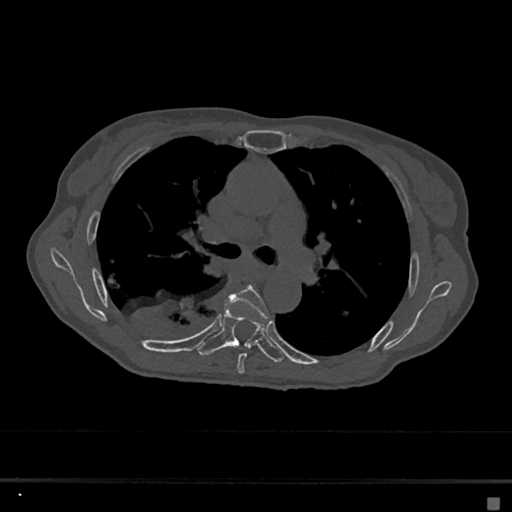
CT including the spine, one axial slice; slice 437 of 797 in the series (ordered by position); reconstruction kernel Br40s/3; 120 kVp; bone window (W 1800 / L 400 HU); 0.5 mm slice thickness; 512 × 512 image matrix, field of view 360 × 360 mm. Female patient, age 68 years. Case-level facts recorded for this patient, not image findings: primary cancer: renal.
Outlined on this slice (semi-automatically segmented with operator editing):
- T5 vertebra: bounding box <226,285,269,374> (left, top, right, bottom; pixels)
- T6 vertebra: <197,303,284,363>